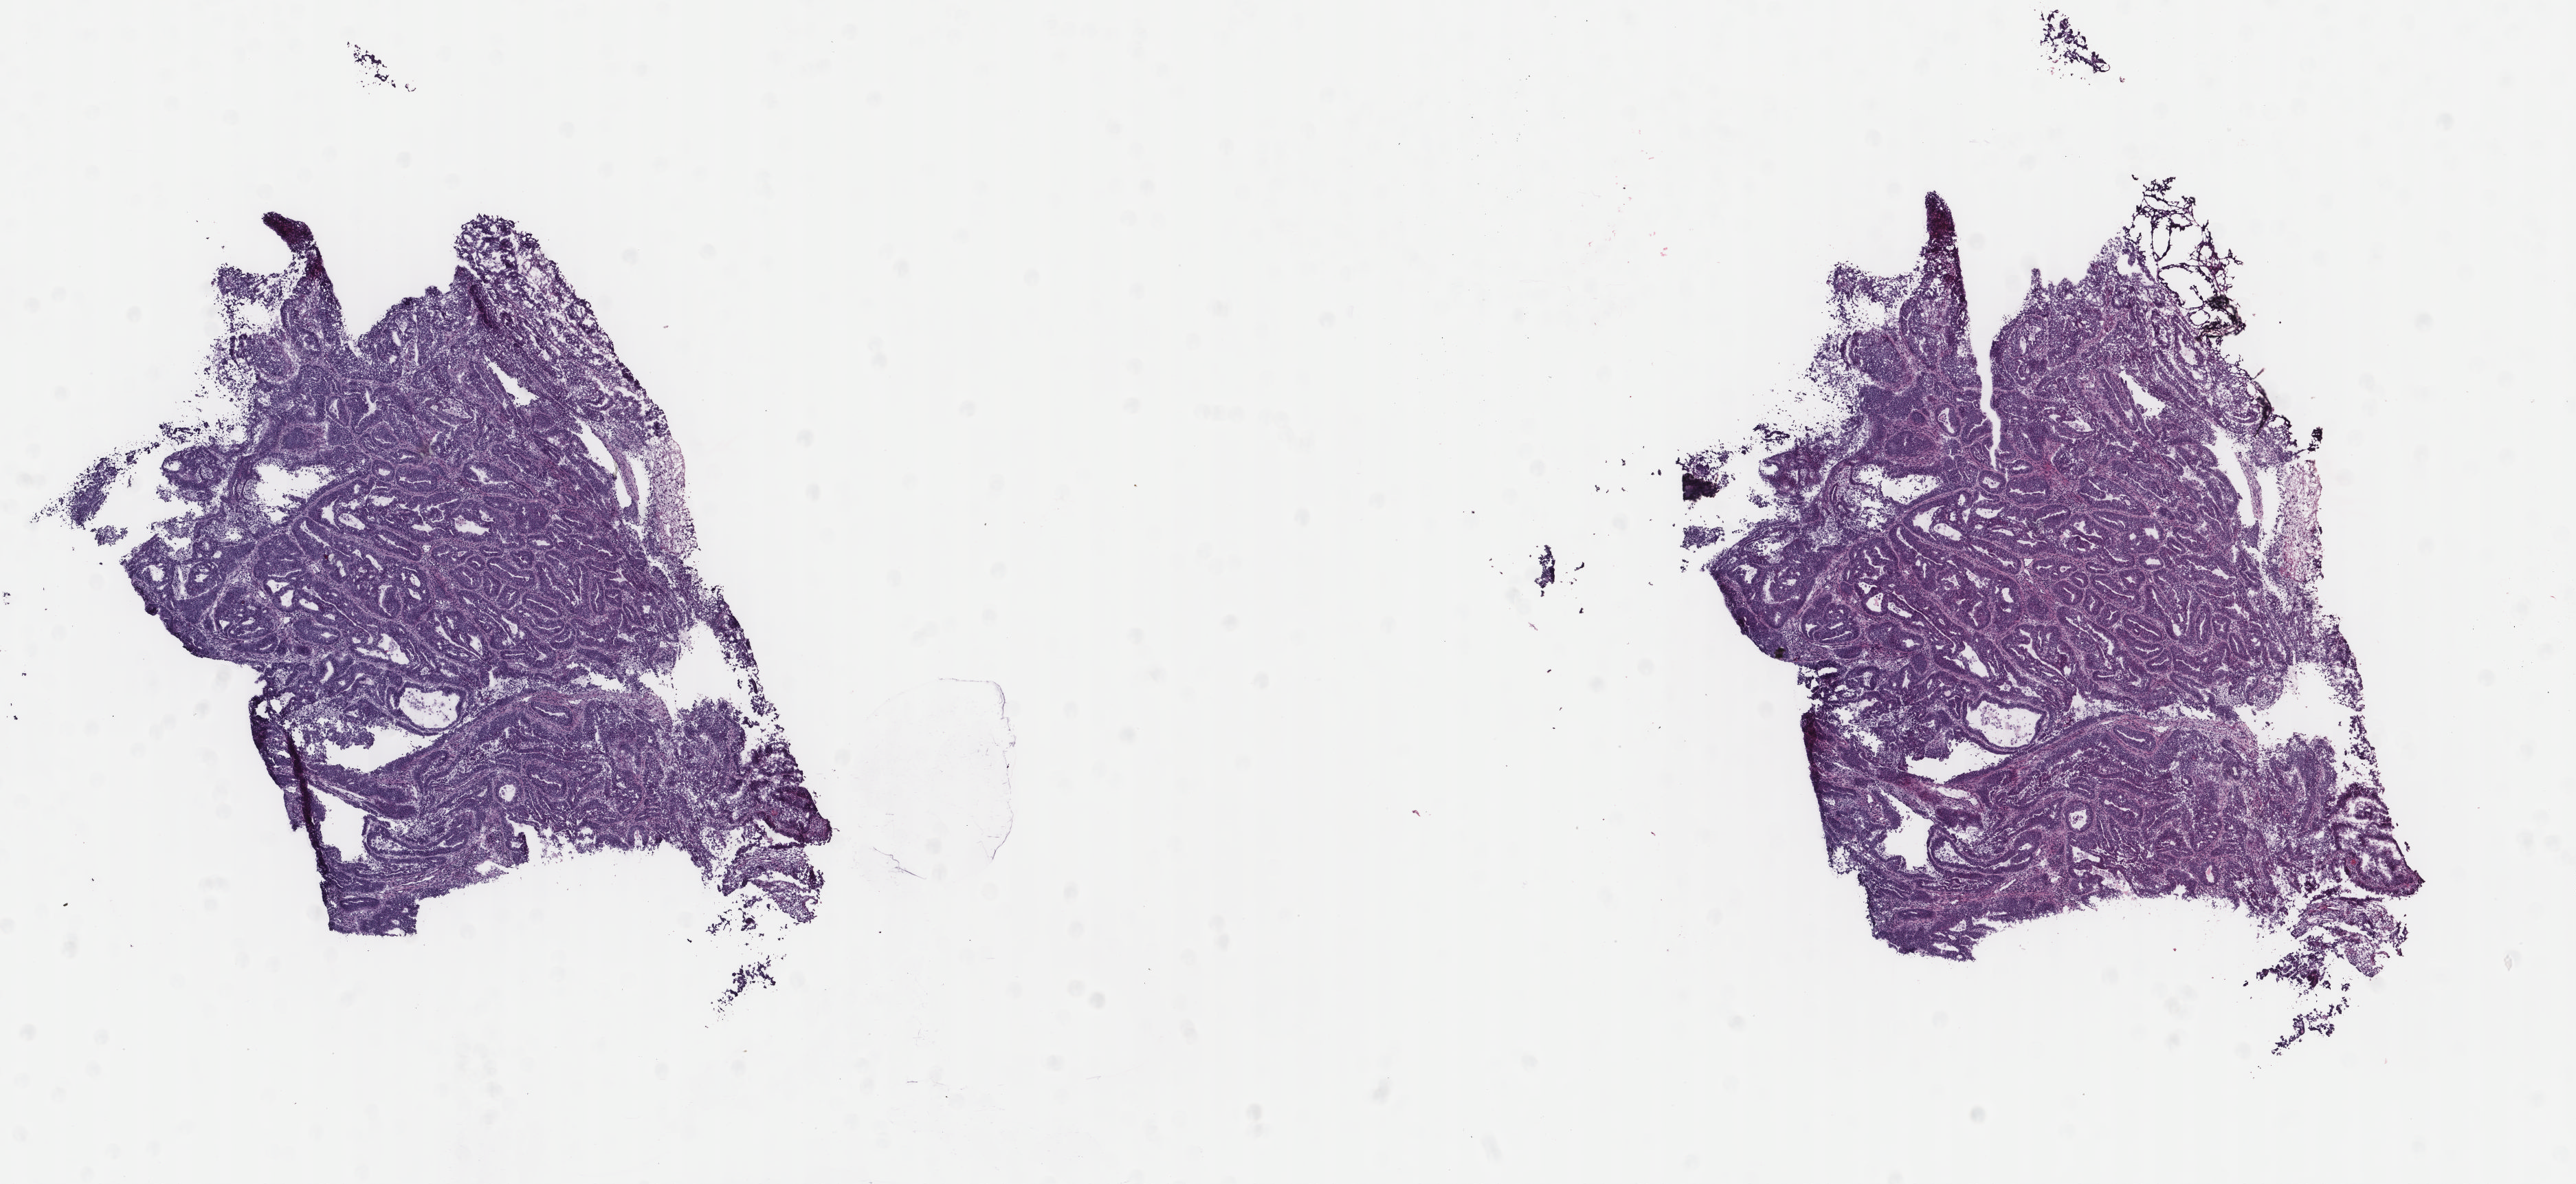
H&E-stained whole-slide image — shown as a low-resolution overview of the whole scanned area (about 14.9 x 6.8 mm, acquisition: 40x scan), frozen section from the top of the tissue portion, primary tumour sample from the uterus. Patient: female, age at initial diagnosis 65 years. Histologic grade: G2 (moderately differentiated). Slide review estimates, as recorded: tumour cells 100%, tumour nuclei 70%, normal cells 0%, stromal cells 0%, necrosis 0%. Infiltration values recorded for this section: lymphocyte infiltration 0%, monocyte infiltration 0%, neutrophil infiltration 0%.
Diagnosis: Endometrioid adenocarcinoma, NOS (endometrium). FIGO stage: IB.